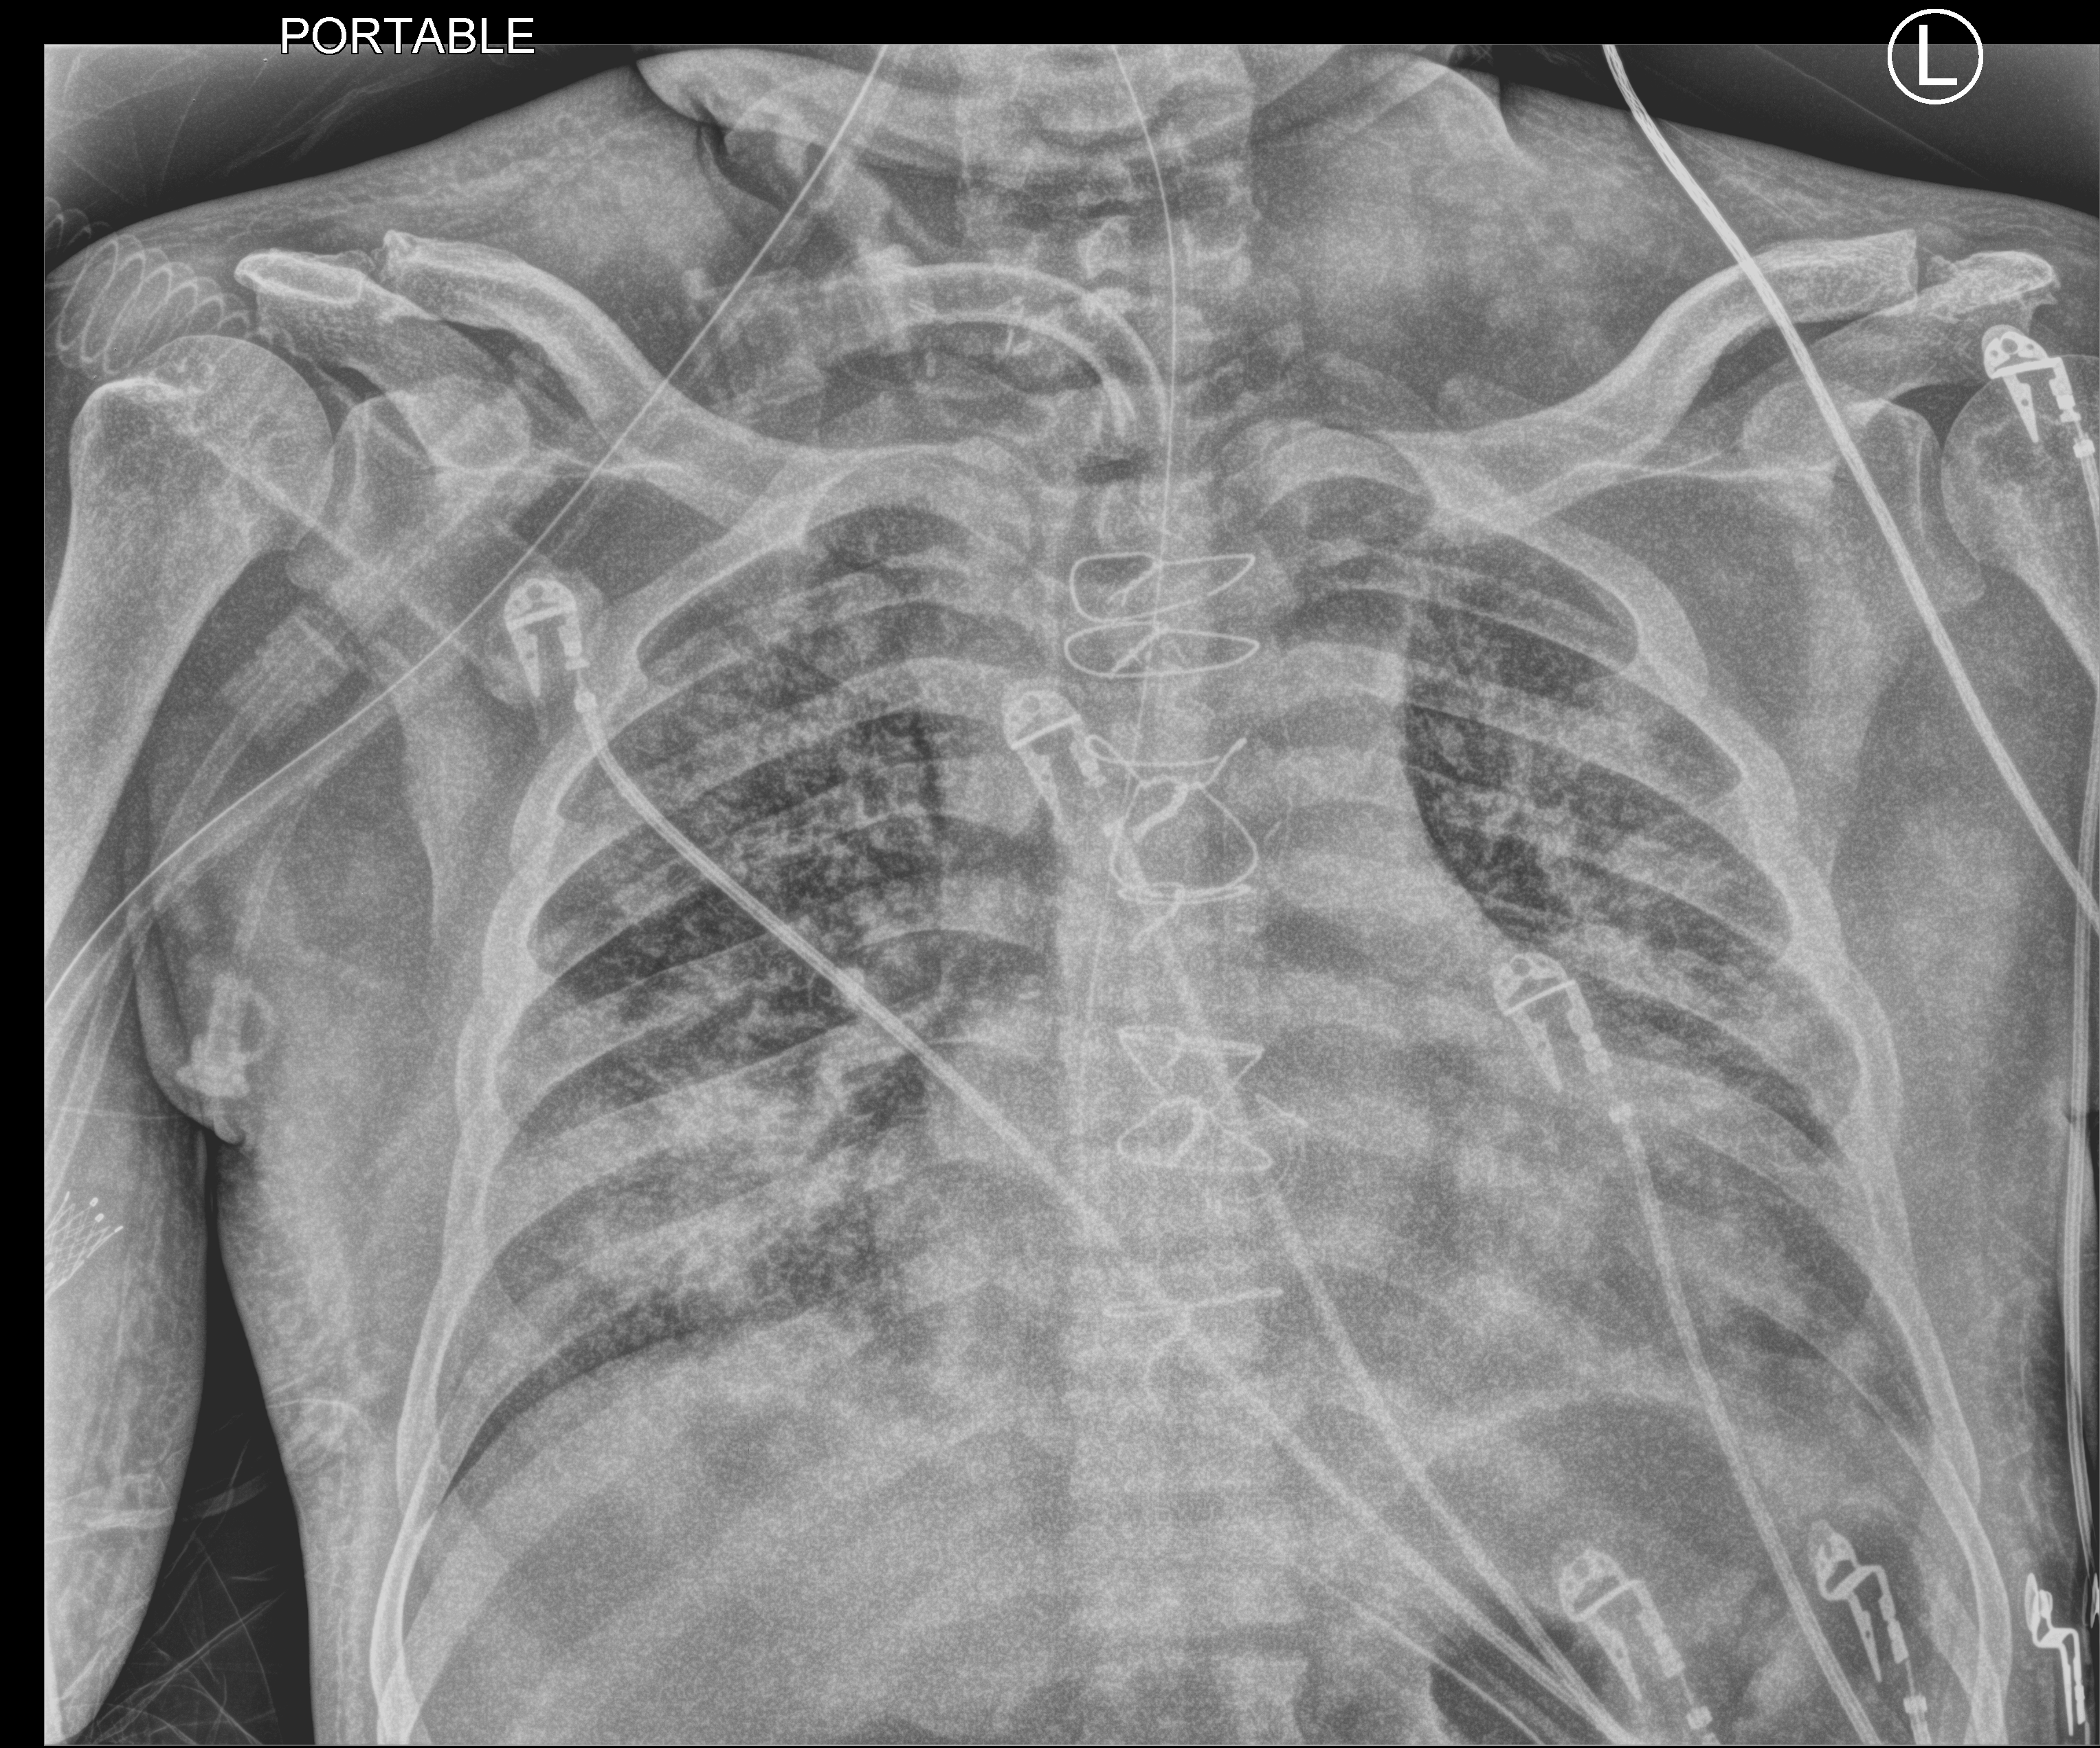
Bedside chest radiograph (computed radiography); anteroposterior (AP) projection. Patient hospitalised with COVID-19; male, aged 60–74 years.
Hospital-stay facts (about this admission, not read from this image; timing relative to this image not recorded): hypertension (admission record): no.